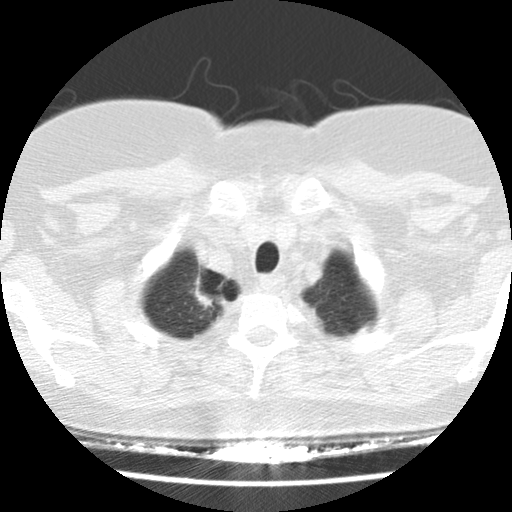
Low-dose screening chest CT, axial slice. Baseline annual screen. Lung window (W 1500 / L -600 HU). 2.5 mm slice thickness. Female, age 58 years at enrolment. Former smoker at enrolment.
Expert reader's lesion annotation, bounding box (x1, y1, x2, y2) in pixels: (167, 256, 247, 334). The exam's reader record, not a measurement of the box and not confirmed to be the same lesion: non-calcified nodule or mass ≥4 mm, right upper lobe, 28 × 24 mm, spiculated (stellate) margins, soft tissue attenuation. Lung cancer was diagnosed 40 days after this screen: adenocarcinoma, NOS, right upper lobe, poorly differentiated (G3), stage IB (AJCC 6th edition), 29 mm at pathology.